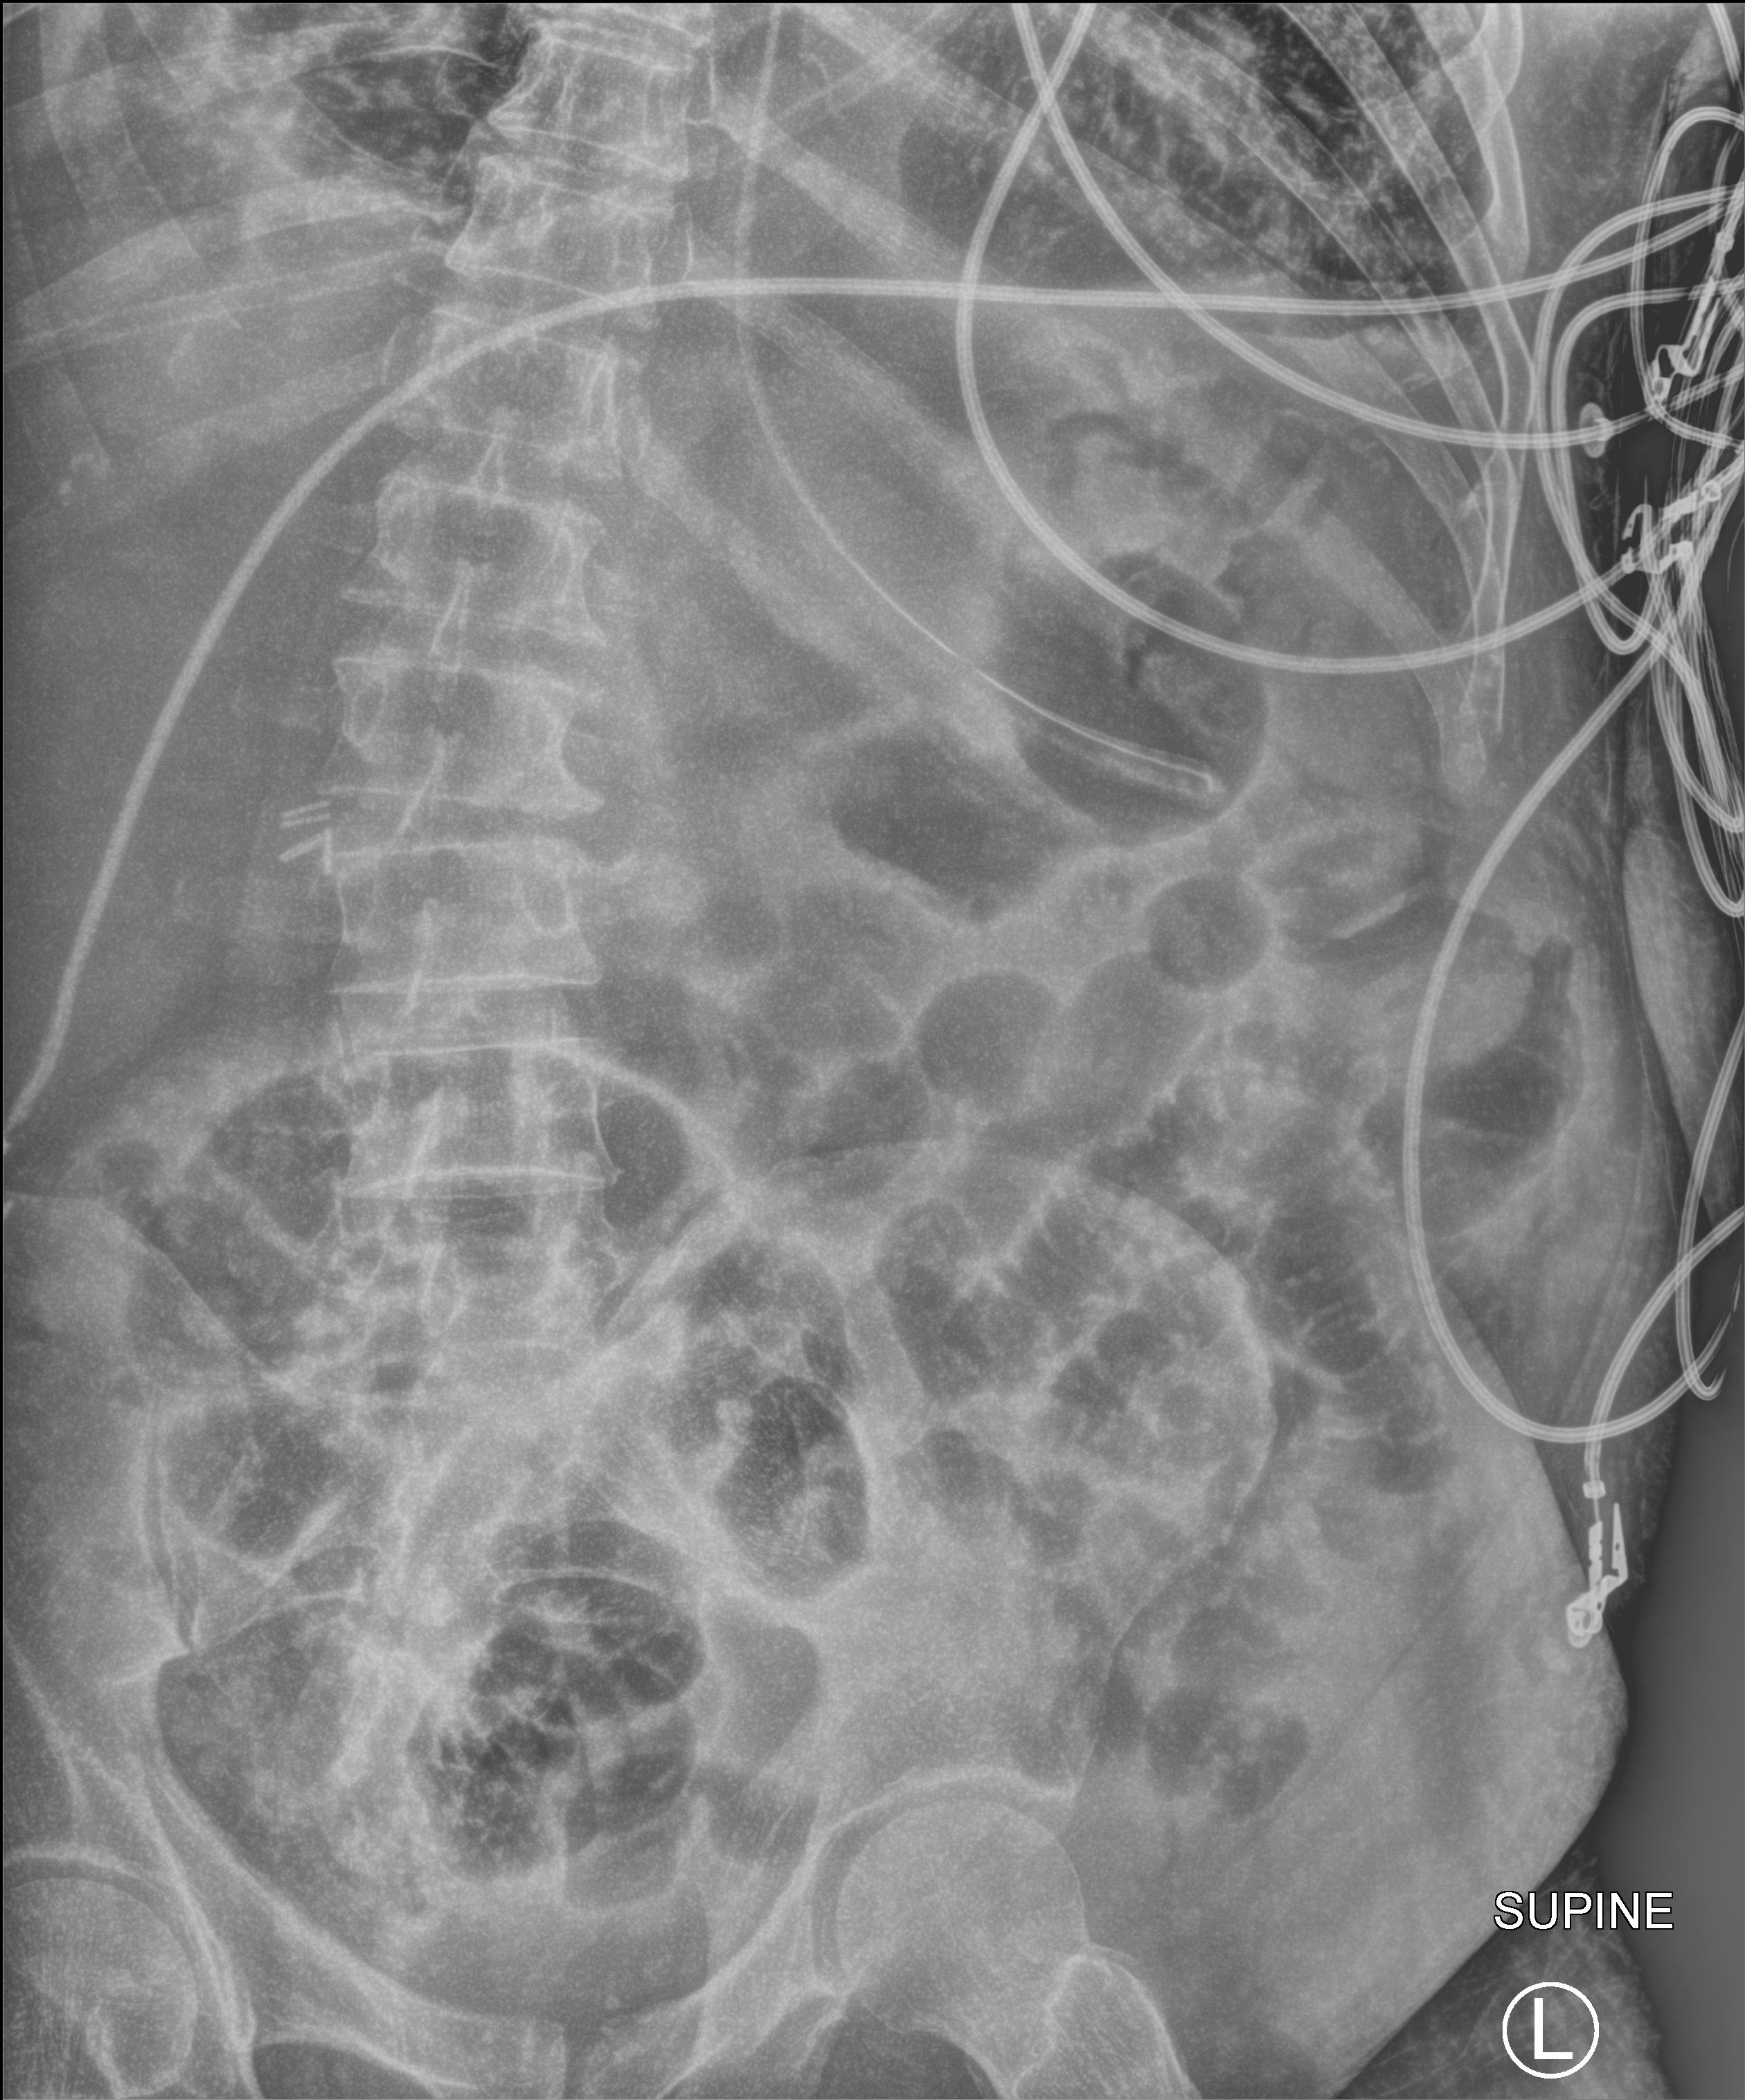
Abdomen X-ray (portable), anteroposterior (AP) projection. Patient hospitalised with COVID-19; male, aged 75–90 years.
Hospital-stay facts (about this admission, not read from this image; timing relative to this image not recorded):
- mechanically ventilated during this hospital stay: yes